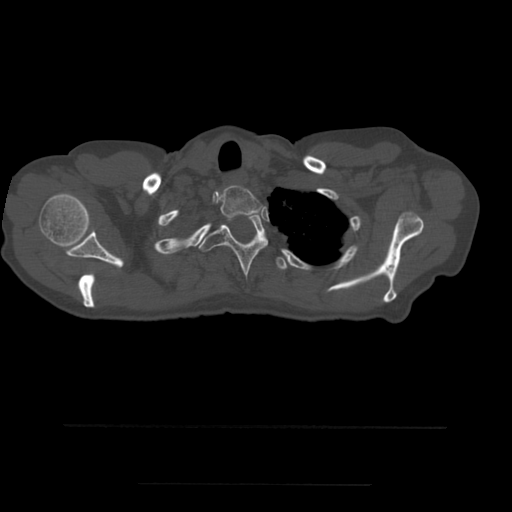
CT including the spine, one axial slice; slice 436 of 544 in the series (ordered by position); bone window (W 1800 / L 400 HU); 512 × 512 image matrix, field of view 350 × 350 mm. Patient age 58 years. From the clinical record (not read from this slice): primary cancer: lung.
Structures marked on this image (semi-automatic segmentation, software-assisted and operator-edited):
- T1 vertebra: box from (x=219, y=184) to (x=263, y=219) px
- T2 vertebra: (x=199, y=213)–(x=268, y=276)
- T3 vertebra: (x=276, y=257)–(x=288, y=270)